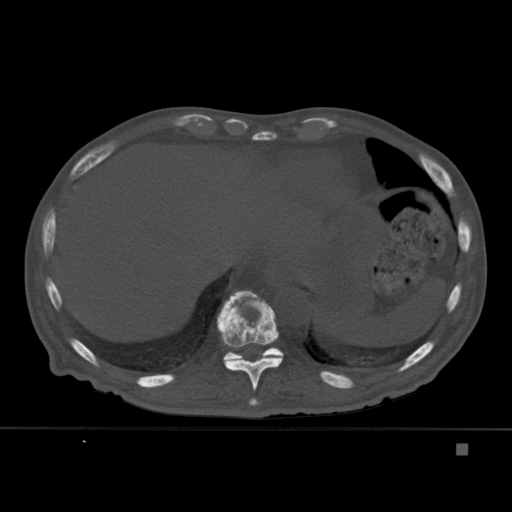
CT including the spine, one axial slice. Position 229 of 451 along the scan axis. Bone window (W 1800 / L 400 HU). 1.5 mm slice thickness. 512 × 512 image matrix, field of view 378 × 378 mm. Patient: male, 75 years. From the clinical record (not read from this slice): primary cancer: prostate.
Outlined on this slice (semi-automatically segmented with operator editing):
- T10 vertebra: bounding box (x1, y1, x2, y2) in pixels: (217, 290, 283, 406)
- T11 vertebra: (221, 298, 284, 361)
- T9 vertebra: (249, 398, 258, 402)